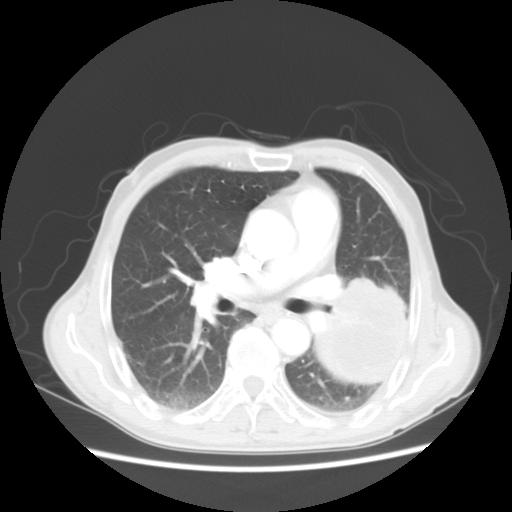
Chest CT, one axial slice. Reconstruction kernel STANDARD. Lung window (W 1500 / L -600 HU). 5 mm slice thickness. 512 × 512 image matrix. Patient: male, 64 years. Case-level facts recorded for this patient, not image findings: clinical TNM (as recorded): T4 N0 M0.
Annotated regions visible in this slice (bounding box drawn by a radiologist):
- lung tumour (recorded histology: squamous cell carcinoma): bounding box [x1, y1, x2, y2] px = [313, 269, 405, 386]